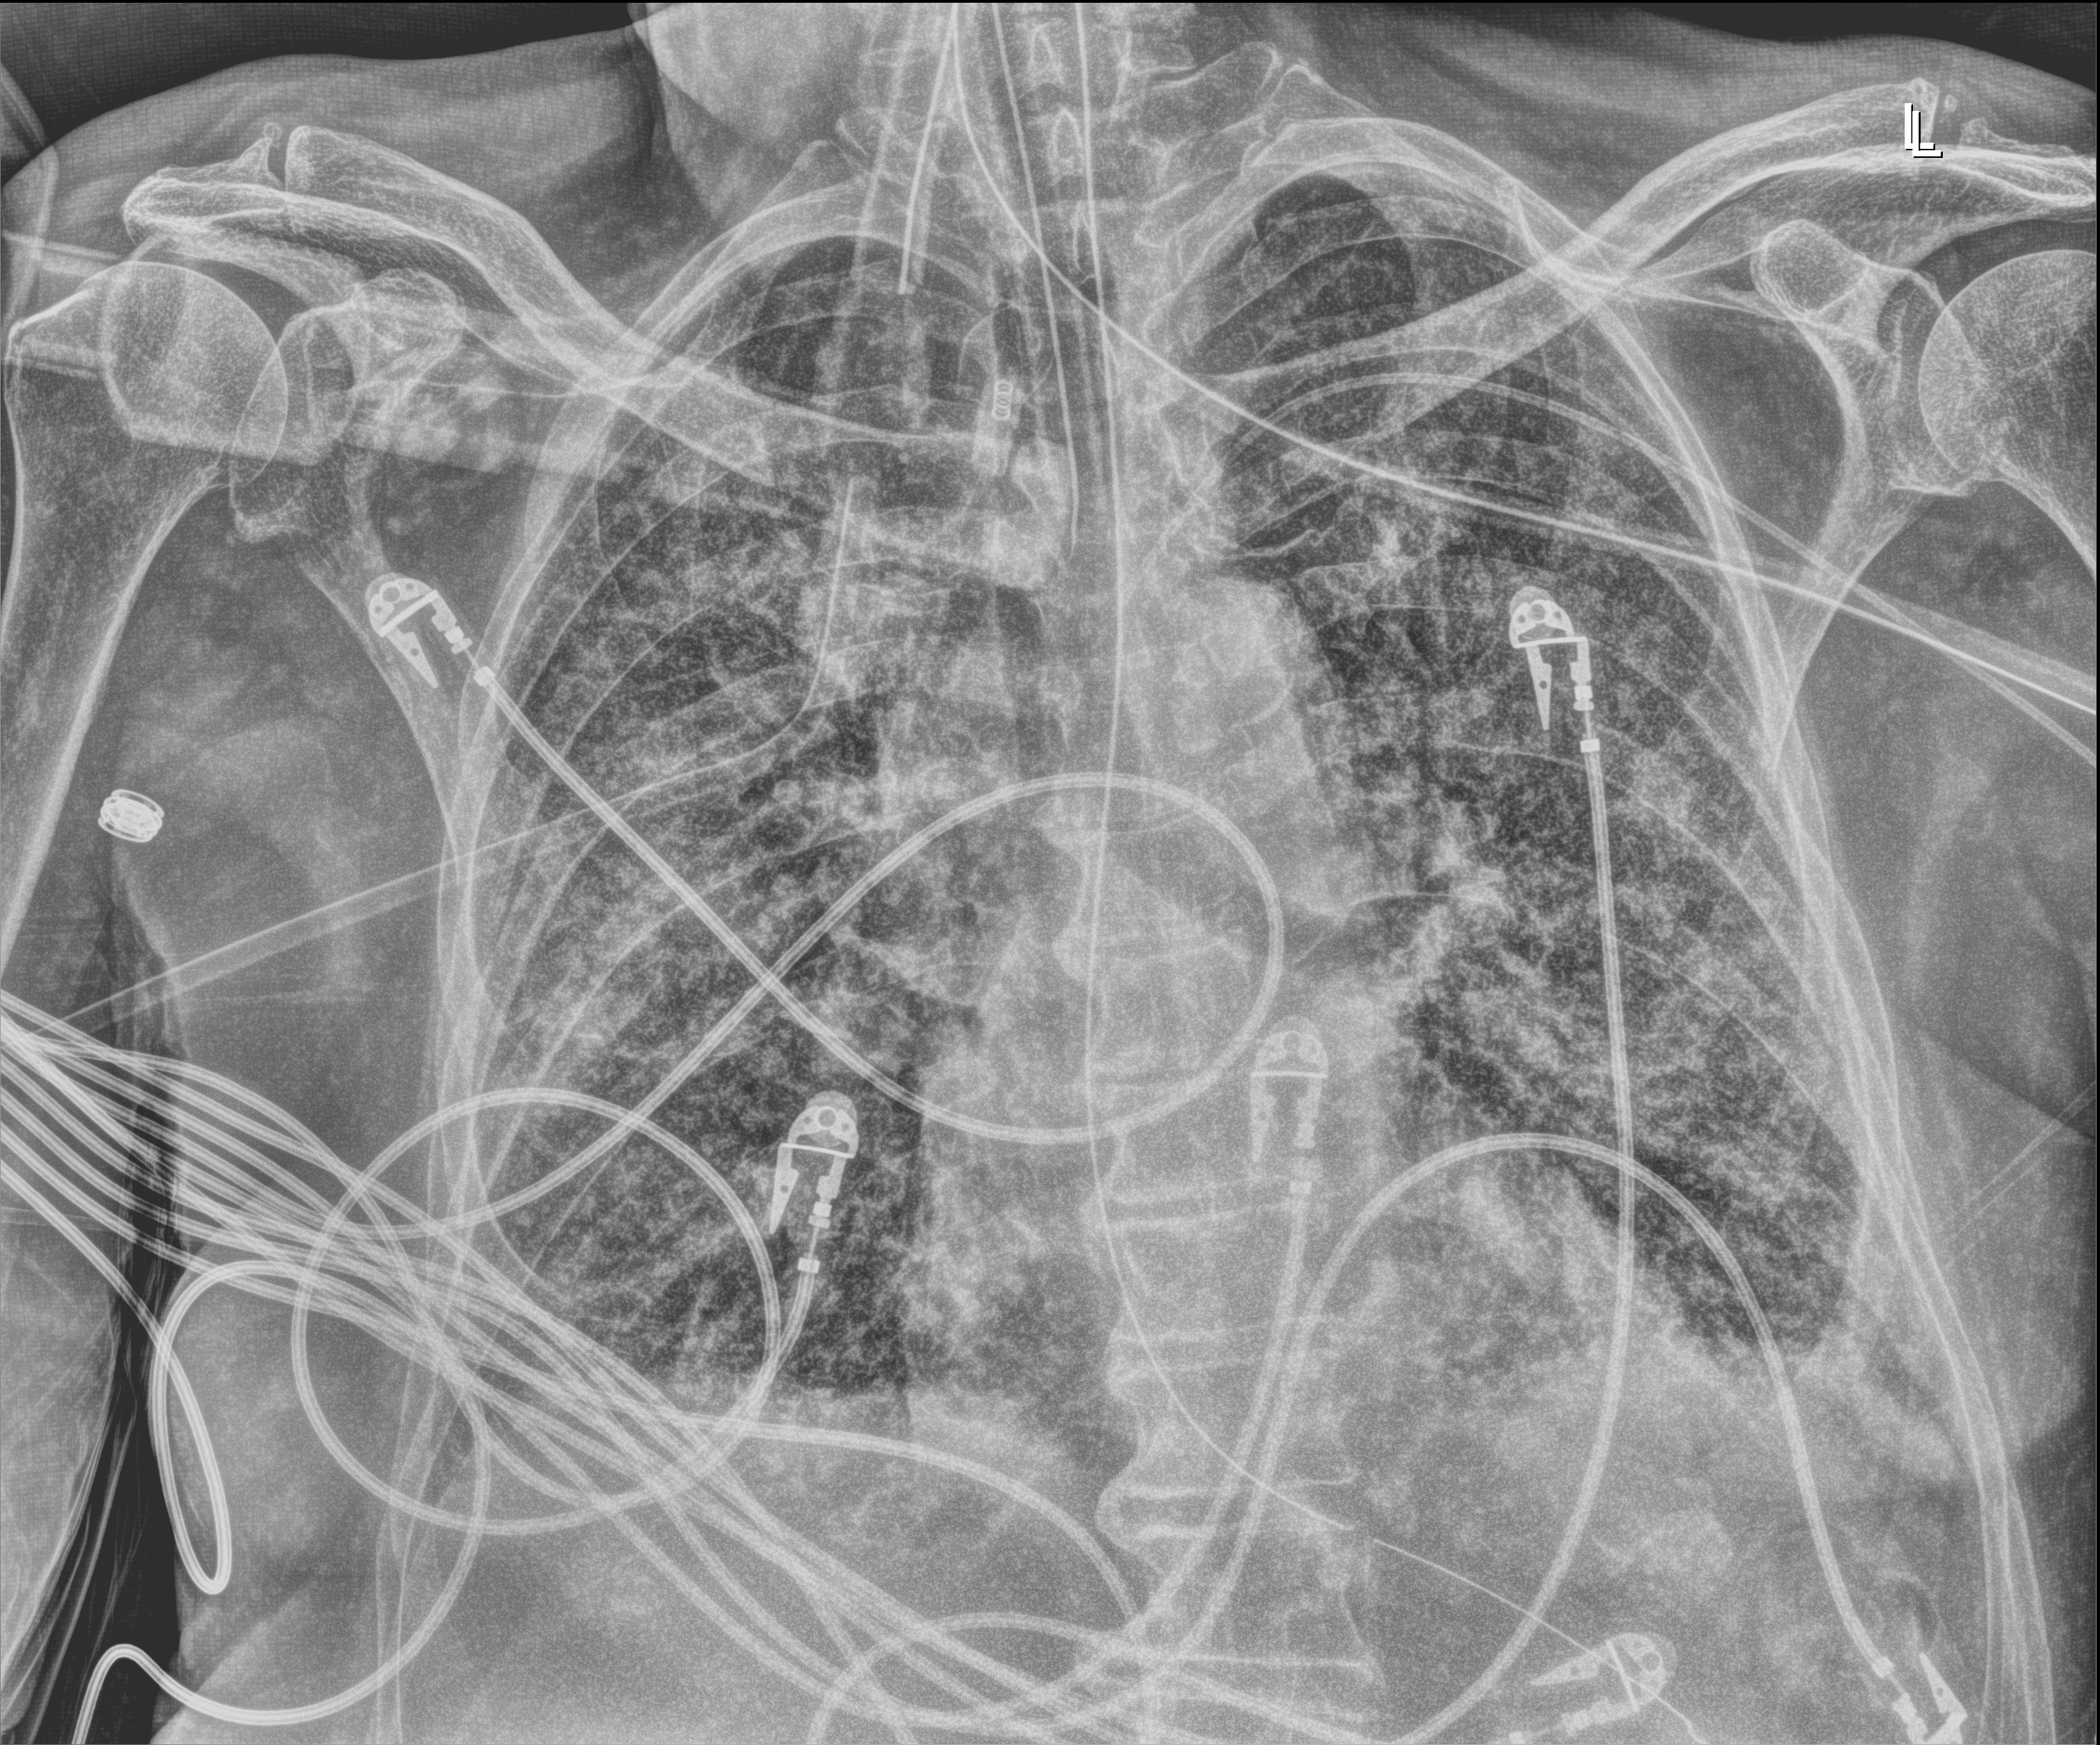
Chest X-ray (portable); anteroposterior (AP) projection. Male patient hospitalised with COVID-19, age 75–90 years.
Hospital-stay facts (about this admission, not read from this image; timing relative to this image not recorded): admitted to intensive care during this hospital stay: yes; COPD (admission record): no; chronic kidney disease (admission record): no.